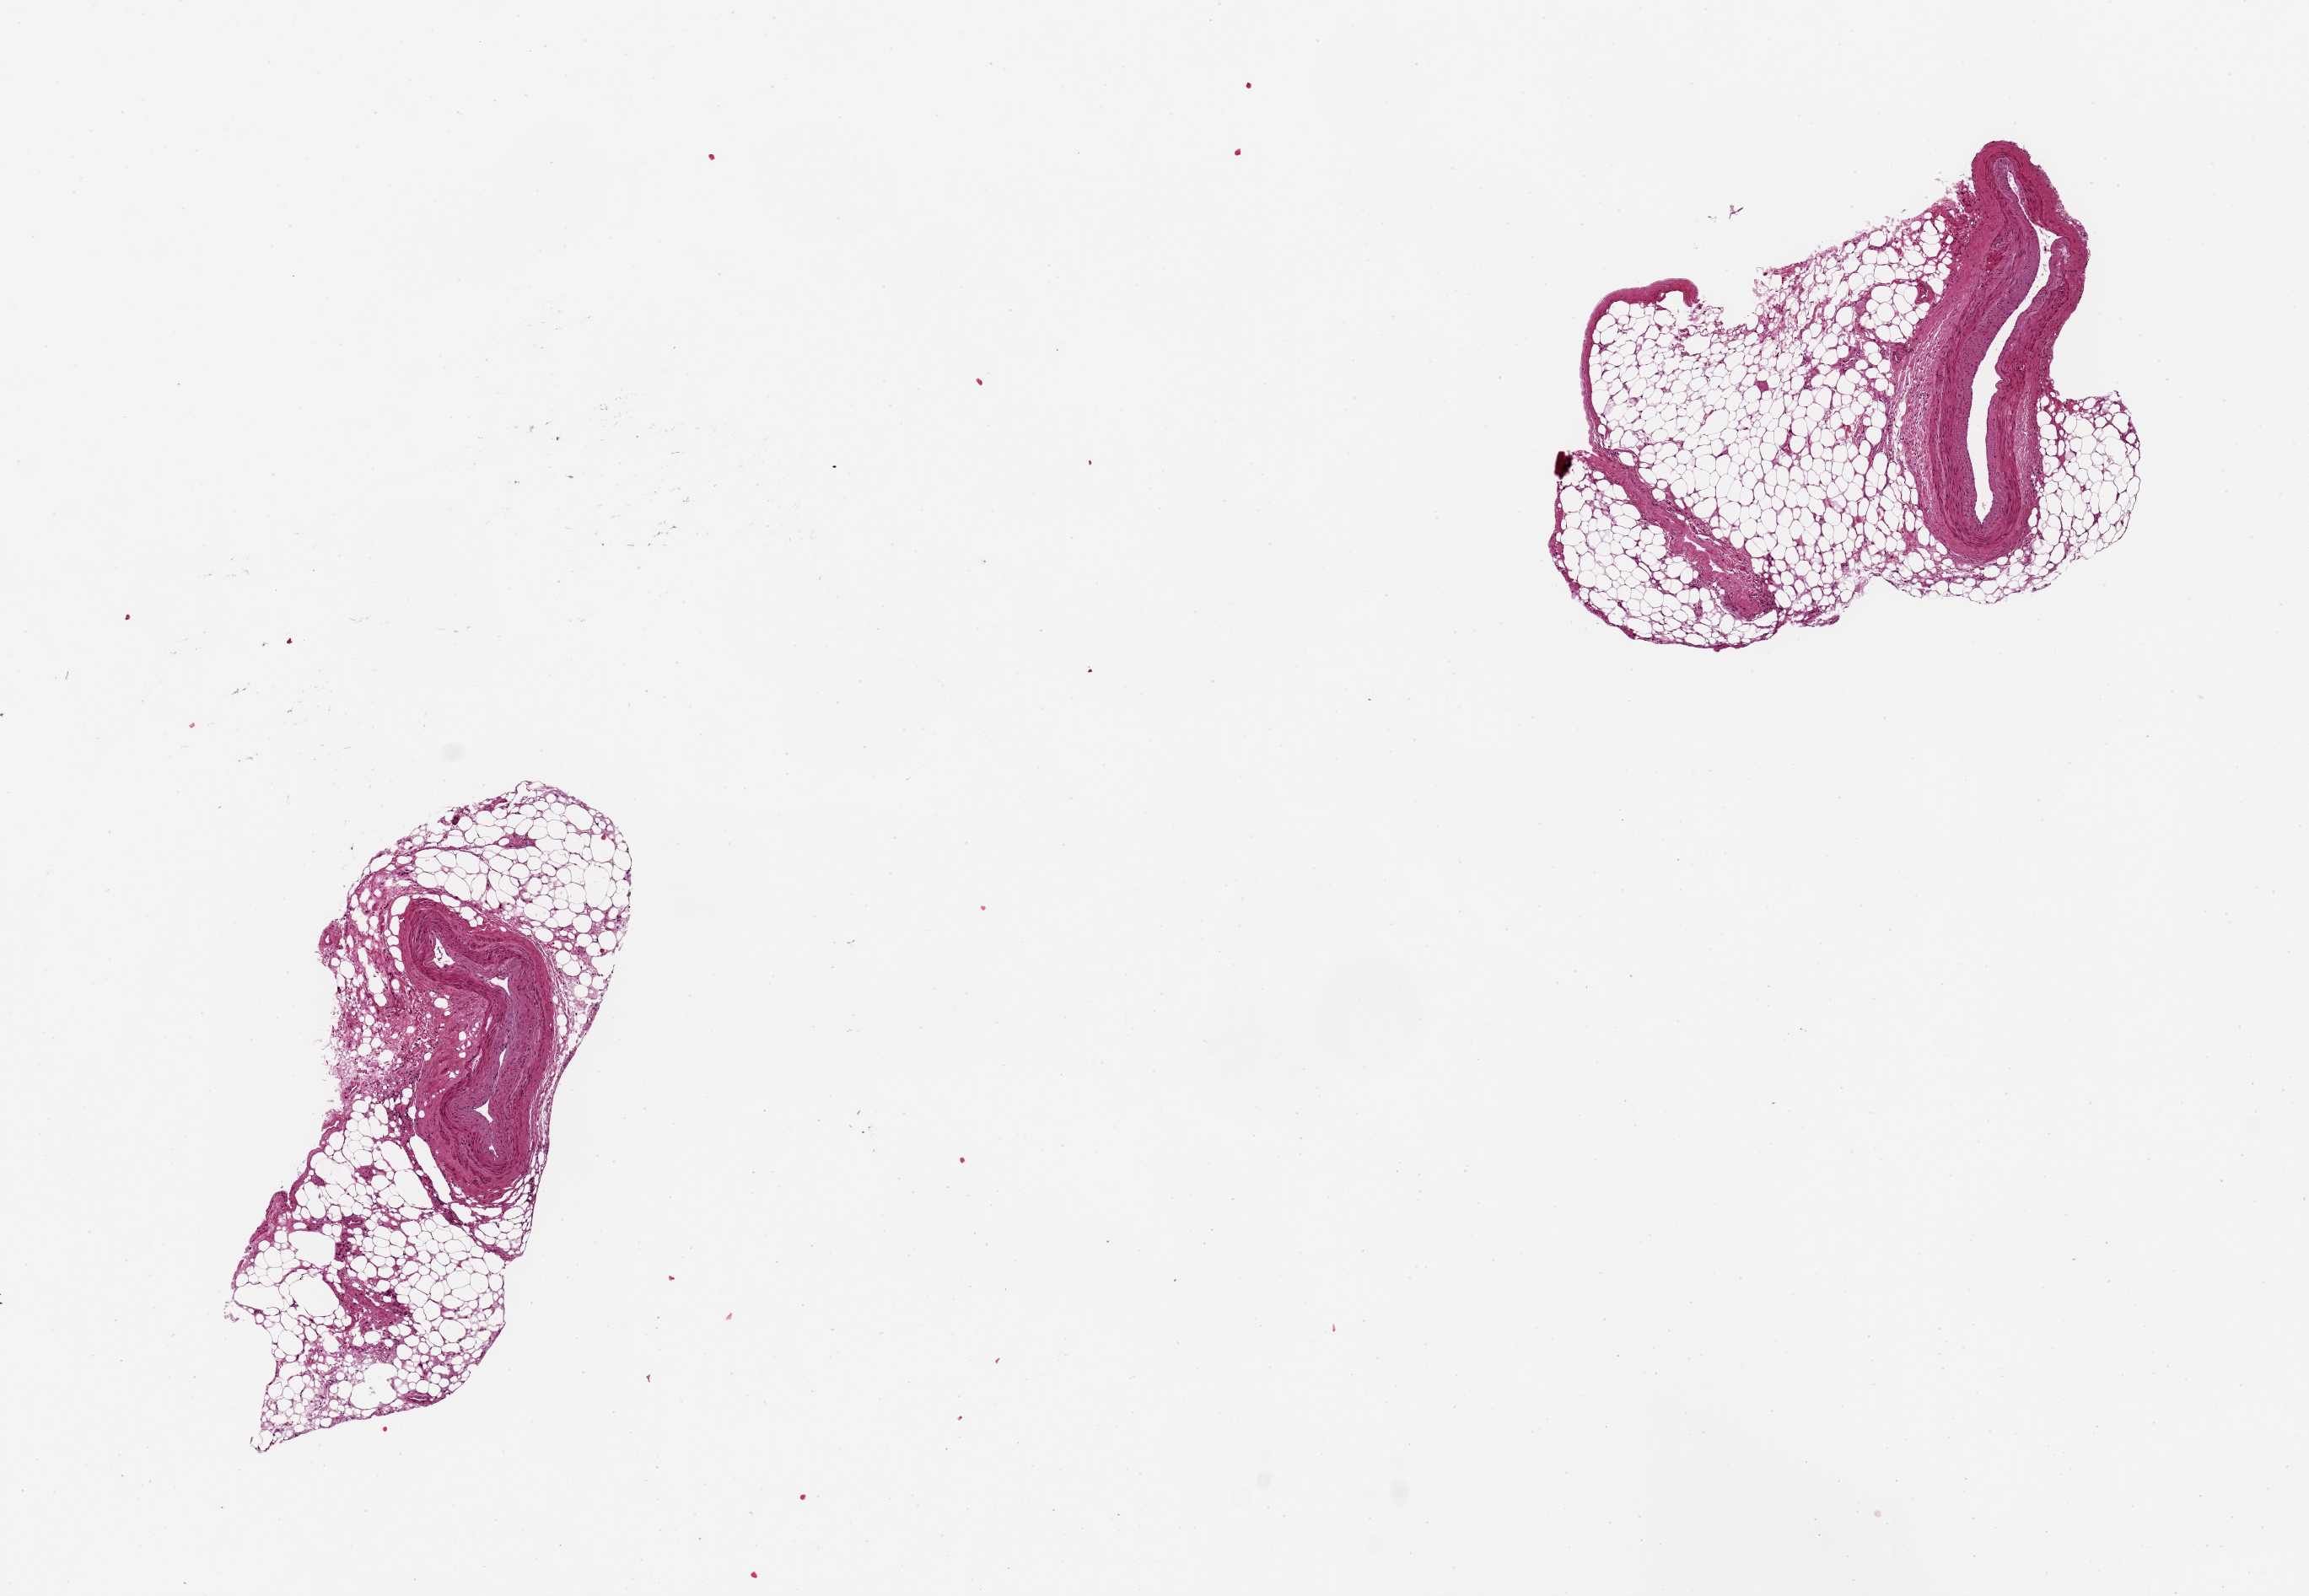
Whole-slide image, hematoxylin and eosin (H&E) stain — shown as a low-resolution overview of the whole scanned area (about 10.8 x 7.5 mm, slide scanned at 20x). Donor sex: female.
Specimen: PAXgene-fixed, paraffin-embedded tissue; sampled site (target tissue): coronary artery; donor tissue sample.